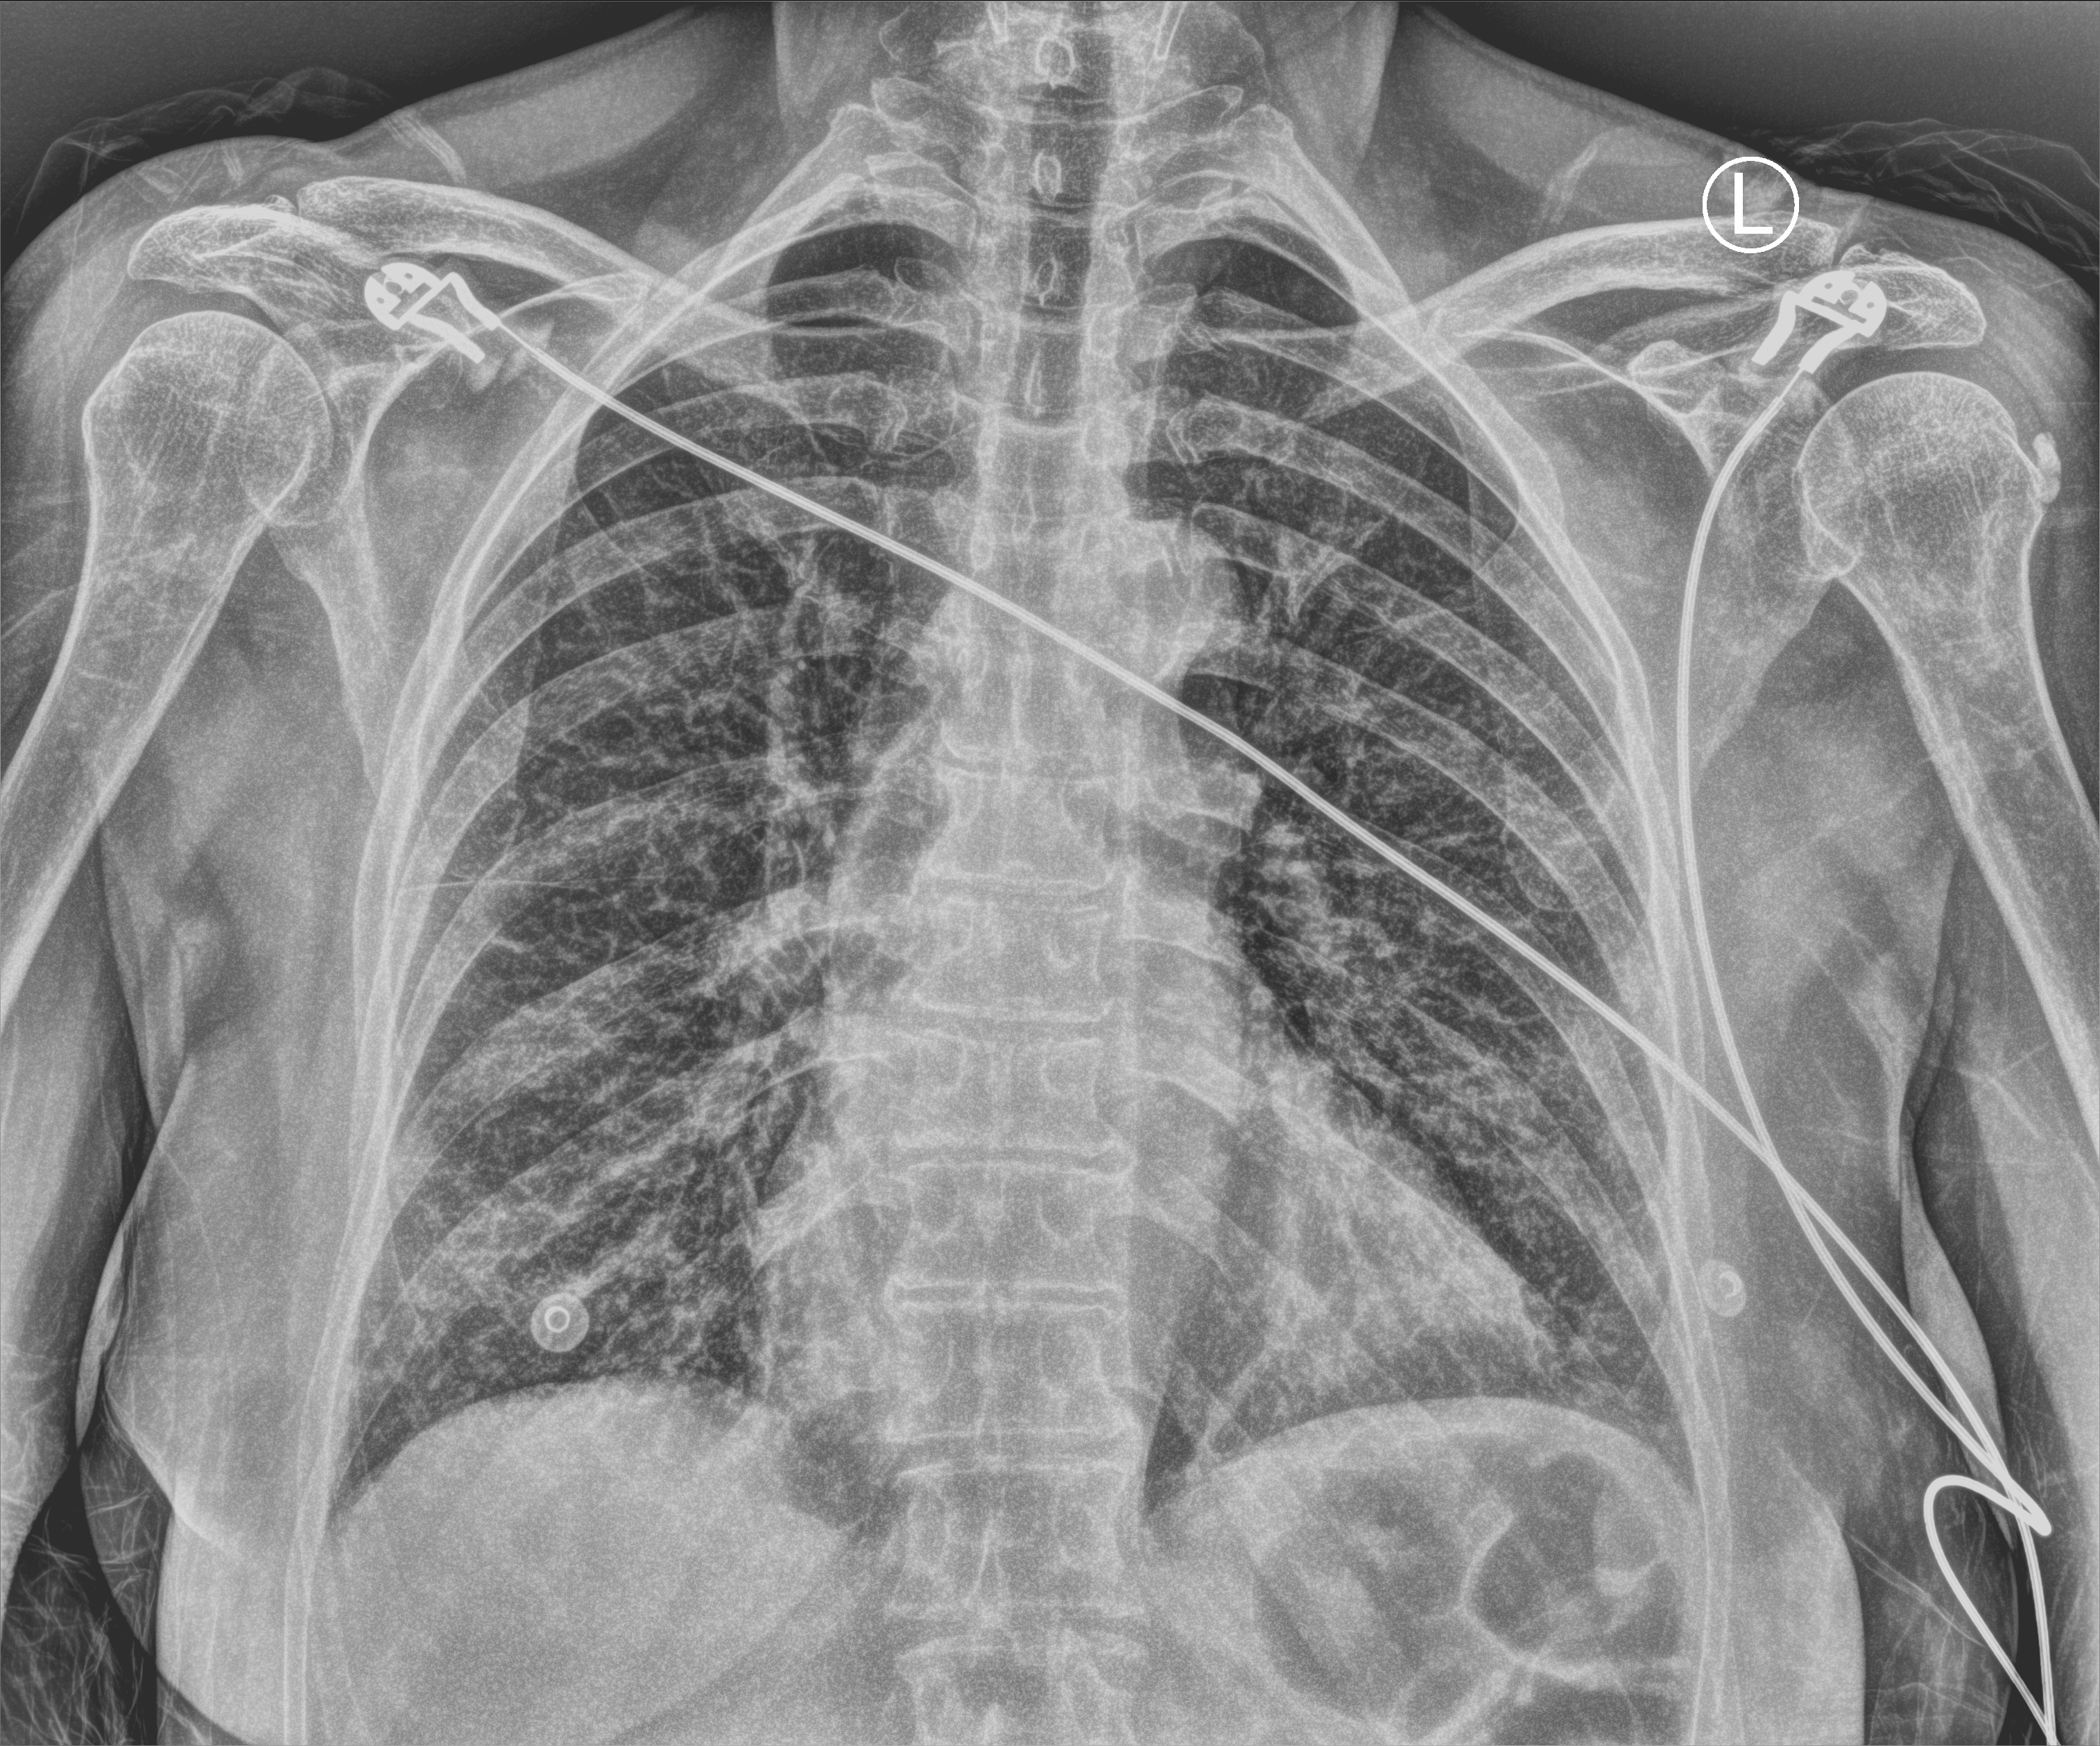
Bedside chest radiograph (computed radiography); anteroposterior (AP) projection. Female patient hospitalised with COVID-19, age 60–74 years.
Hospital-stay facts (about this admission, not read from this image; timing relative to this image not recorded): mechanically ventilated during this hospital stay: no; admitted to intensive care during this hospital stay: no.